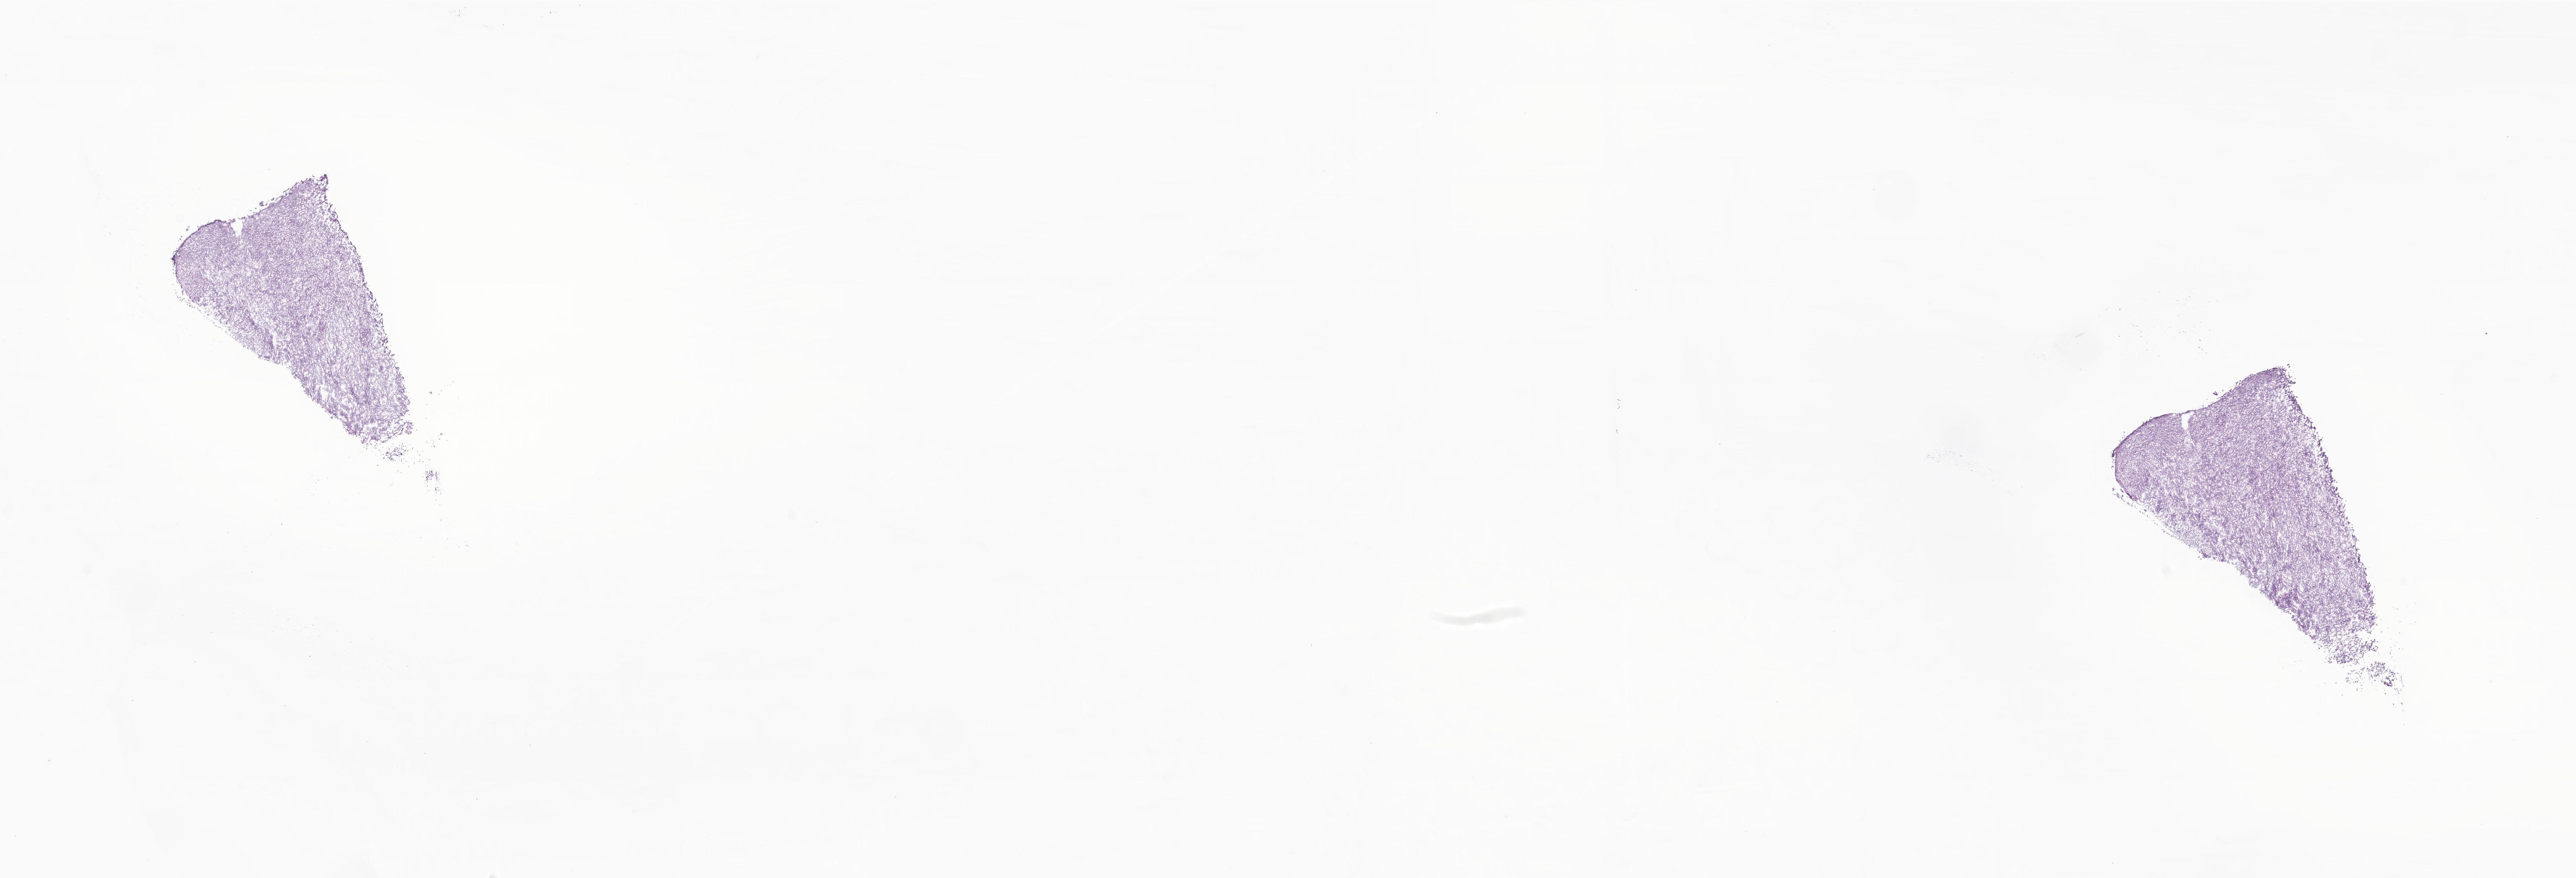
Digitized H&E-stained section of tumor tissue from the brain — whole scanned area (about 27.6 x 9.4 mm) shown as a low-resolution overview. Cryosection (OCT / tissue freezing medium). Patient female; age 46 months (3 years 10 months).
Recorded diagnosis: Neoplasm, malignant.